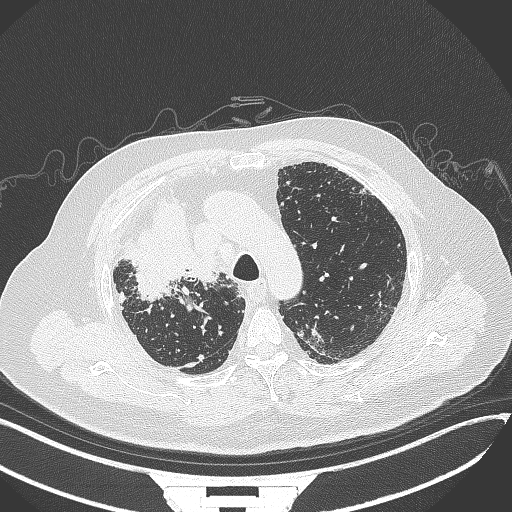
Chest CT, one axial slice; slice 267 of 384 in the series (ordered by position); reconstruction kernel B70f; 120 kVp; lung window (W 1500 / L -600 HU); 1 mm slice thickness; 512 × 512 image matrix. Male patient, age 69 years. Case-level facts recorded for this patient, not image findings: clinical TNM (as recorded): T4 N3 M1.
Outlined on this slice (bounding box drawn by a radiologist):
- lung tumour (recorded histology: adenocarcinoma): bounding box <127,193,216,304> (left, top, right, bottom; pixels)